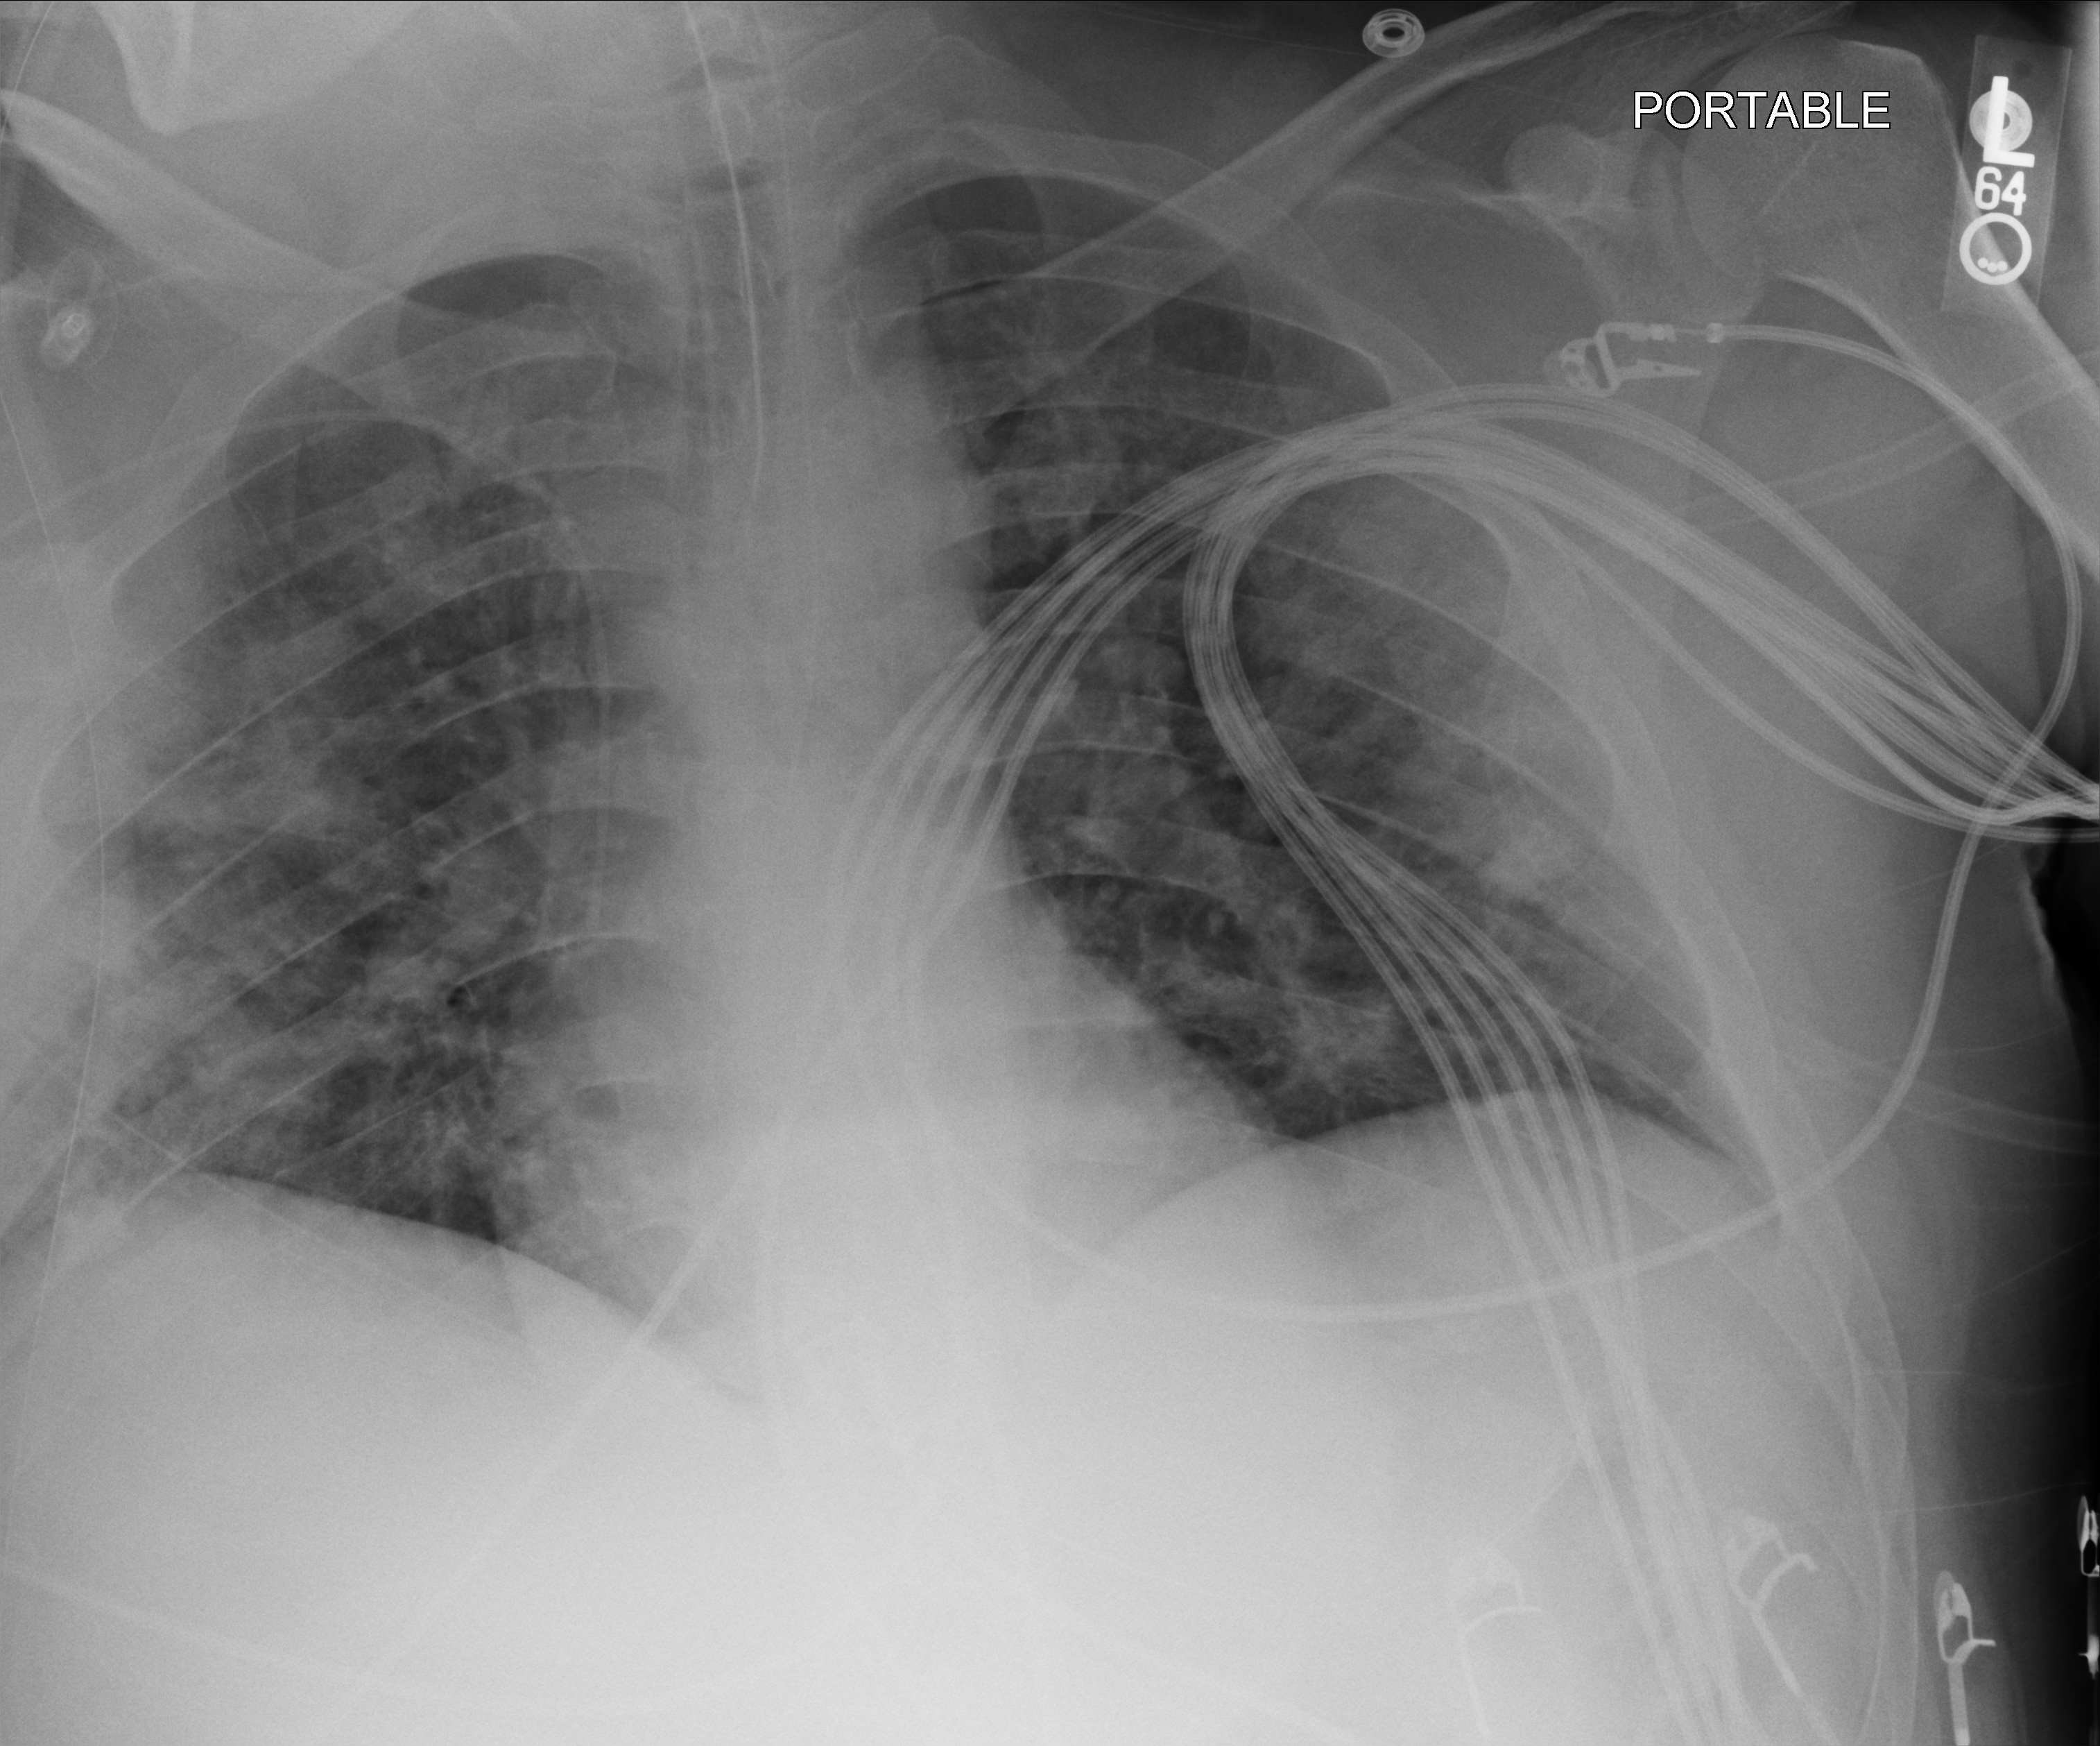
Portable chest radiograph, anteroposterior (AP) projection. Patient hospitalised with COVID-19; female, aged 18–59 years.
Hospital-stay facts (about this admission, not read from this image; timing relative to this image not recorded): chronic kidney disease (admission record): no; admitted to intensive care during this hospital stay: yes; mechanically ventilated during this hospital stay: yes.